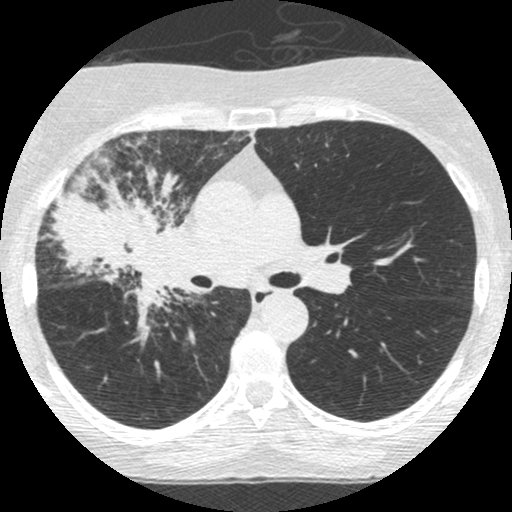
Low-dose screening chest CT, one axial slice; slice 155 of 253 in the series (ordered by position); lung window (W 1500 / L -600 HU); 1.25 mm slice thickness; 512 × 512 image matrix, field of view 294 × 294 mm.
Outlined on this slice (manually delineated by an expert):
- lesion 2 (tumor, hilum of right lung): box from (x=48, y=172) to (x=180, y=308) px